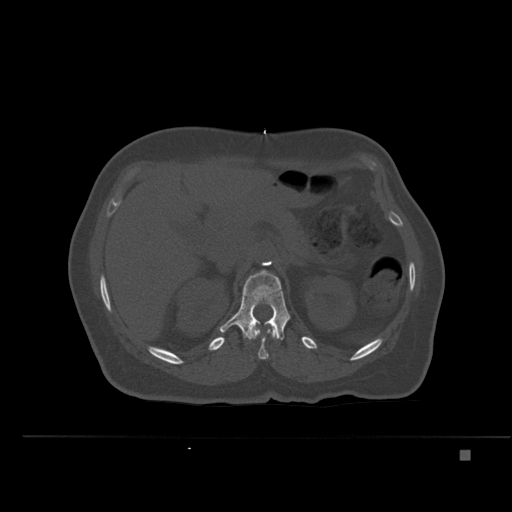
CT including the spine, one axial slice. Slice 240 of 477 in the series (ordered by position). Bone window (W 1800 / L 400 HU). 512 × 512 image matrix, field of view 422 × 422 mm. Female patient, age 74 years. Case-level facts recorded for this patient, not image findings: primary cancer: colon.
Annotated regions visible in this slice (semi-automatically segmented with operator editing):
- L1 vertebra: bounding box (x1, y1, x2, y2) in pixels: (219, 270, 290, 340)
- T12 vertebra: (249, 325, 276, 360)